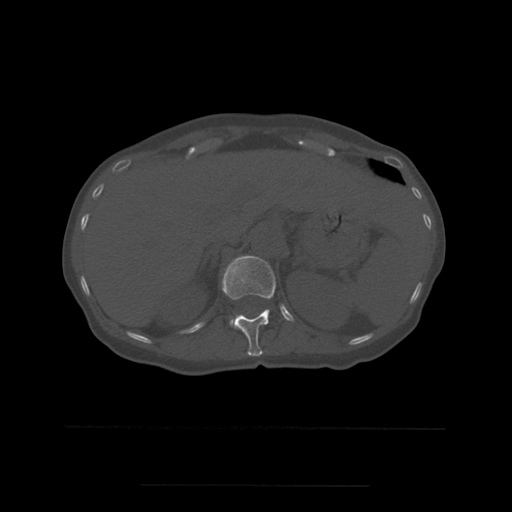
CT including the spine, one axial slice. Slice 254 of 544 in the series (ordered by position). Bone window (W 1800 / L 400 HU). 1.25 mm slice thickness. 512 × 512 image matrix, field of view 350 × 350 mm. Patient age 58 years. Case-level facts recorded for this patient, not image findings: primary cancer: lung.
Outlined on this slice (semi-automatically segmented with operator editing):
- L1 vertebra: bounding box <230,318,236,328> (left, top, right, bottom; pixels)
- T12 vertebra: <222,256,276,357>